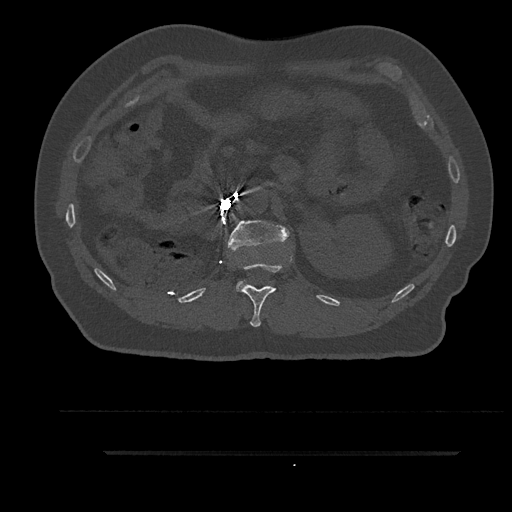
CT including the spine, one axial slice. Position 214 of 797 along the scan axis. Reconstruction kernel Br40s/3. 120 kVp. Bone window (W 1800 / L 400 HU). 0.5 mm slice thickness. 512 × 512 image matrix, field of view 432 × 432 mm. Male patient, age 63 years. From the clinical record (not read from this slice): primary cancer: renal; vertebrae with lytic lesions (as recorded): T8.
Outlined on this slice (semi-automatically segmented with operator editing):
- L1 vertebra: box from (x=228, y=220) to (x=290, y=291) px
- T12 vertebra: (x=240, y=255)–(x=292, y=327)